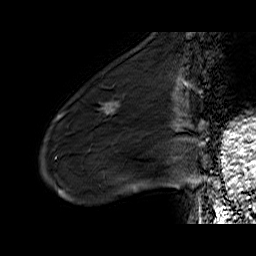
Breast MRI (dynamic contrast-enhanced), one sagittal slice. Position 17 of 60 along the scan axis. Dynamic contrast-enhanced series, time point 2 of 6 at this slice position (early post-contrast). 1.5 T. TE 6.5 ms, TR 32.9 ms. 4 mm slice thickness. 256 × 256 image matrix, field of view 200 × 200 mm. Female patient. Case-level facts recorded for this patient, not image findings: setting: breast cancer imaged before/during neoadjuvant chemotherapy; receptor status: HER2-positive.
Annotated regions visible in this slice (semi-automatically segmented with operator editing):
- analysis volume of interest (the breast-tissue region the enhancement analysis was run in; not a lesion): box from (x=72, y=88) to (x=133, y=137) px
- tumour enhancement mask (voxels above the 100 % enhancement threshold inside the analysis volume of interest): (x=105, y=105)–(x=119, y=114)